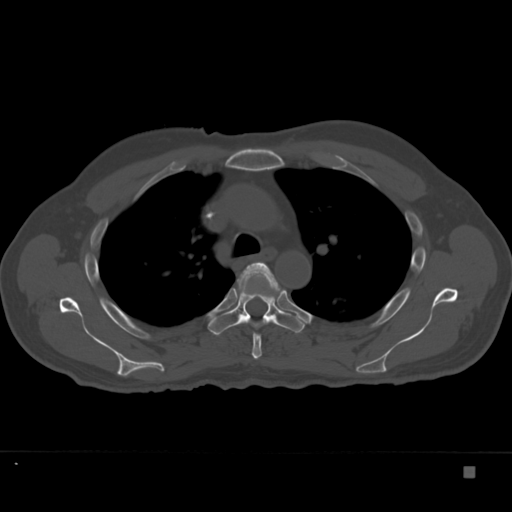
CT including the spine, one axial slice. Slice 262 of 332 in the series (ordered by position). Reconstruction kernel Br40s. 120 kVp. Bone window (W 1800 / L 400 HU). 512 × 512 image matrix, field of view 389 × 389 mm. Patient: male, 72 years. From the clinical record (not read from this slice): primary cancer: skeletal.
Outlined on this slice (semi-automatic segmentation, software-assisted and operator-edited):
- T4 vertebra: box from (x=237, y=262) to (x=282, y=360) px
- T5 vertebra: (x=208, y=265)–(x=305, y=336)